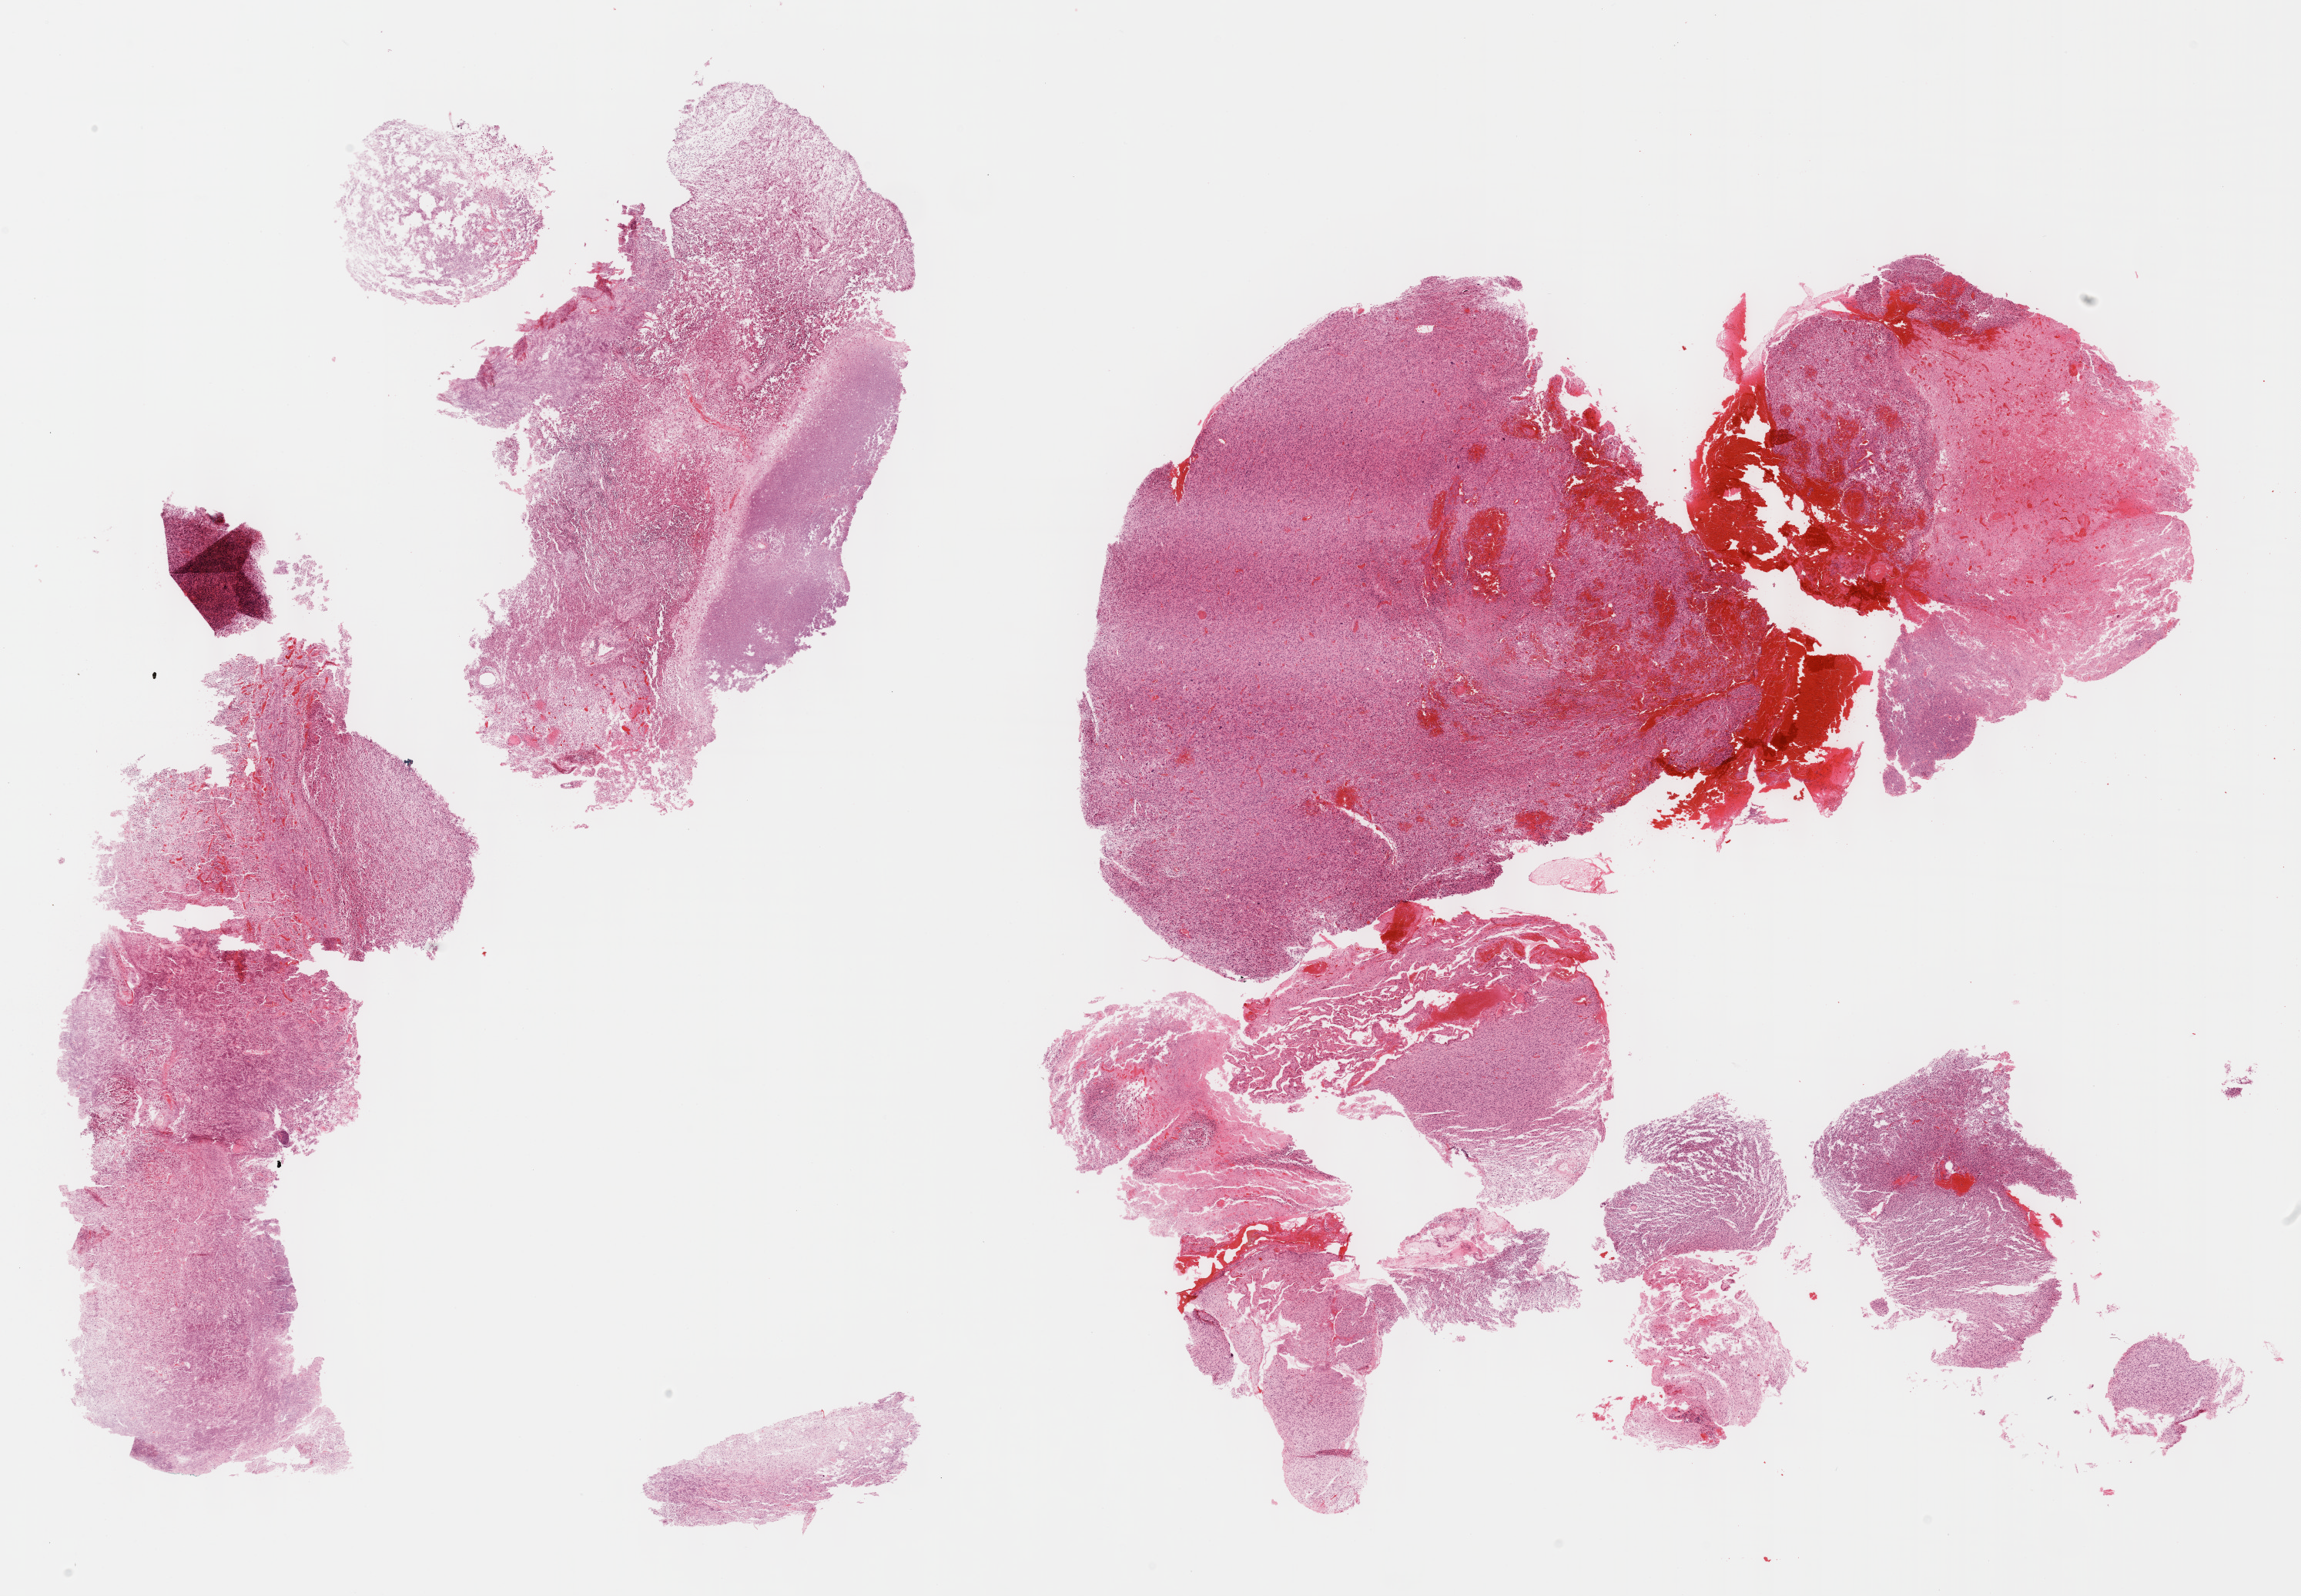
H&E-stained whole-slide image — low-resolution overview of the scanned area, about 24.1 x 16.7 mm (acquisition: 40x scan); formalin-fixed paraffin-embedded (FFPE) diagnostic section; sample: primary tumour, brain. Female, age 30 years at initial diagnosis.
Histologic diagnosis: Glioblastoma.